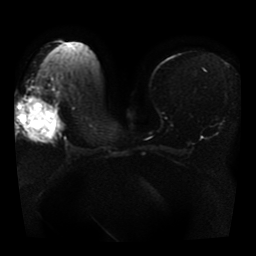
Breast MRI, one axial slice; position 21 of 41 along the scan axis; diffusion-weighted series; image 2 of 4 stored at this slice position (different b-values; order by instance number); 1.5 T; 5 mm slice thickness; 256 × 256 image matrix. Female patient.
Structures marked on this image (expert manual segmentation):
- tumour on diffusion-weighted imaging: box from (x=57, y=124) to (x=66, y=132) px